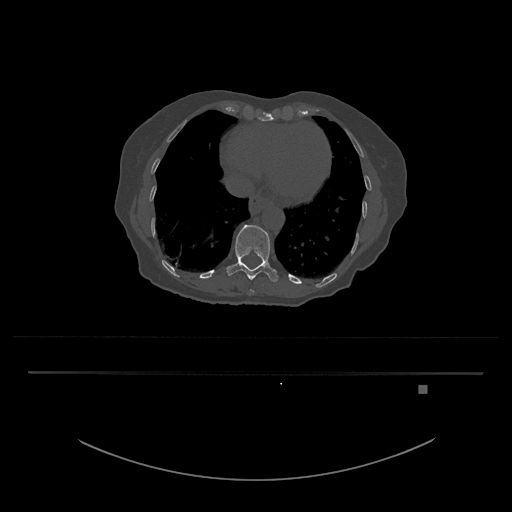
CT including the spine, one axial slice; position 668 of 797 along the scan axis; reconstruction kernel Br40s/3; bone window (W 1800 / L 400 HU); 0.5 mm slice thickness; 512 × 512 image matrix, field of view 500 × 500 mm. Female patient, age 57 years. From the clinical record (not read from this slice): primary cancer: cervical.
Outlined on this slice (semi-automatic segmentation, software-assisted and operator-edited):
- T10 vertebra: bounding box <251,290,254,292> (left, top, right, bottom; pixels)
- T11 vertebra: <226,225,278,282>